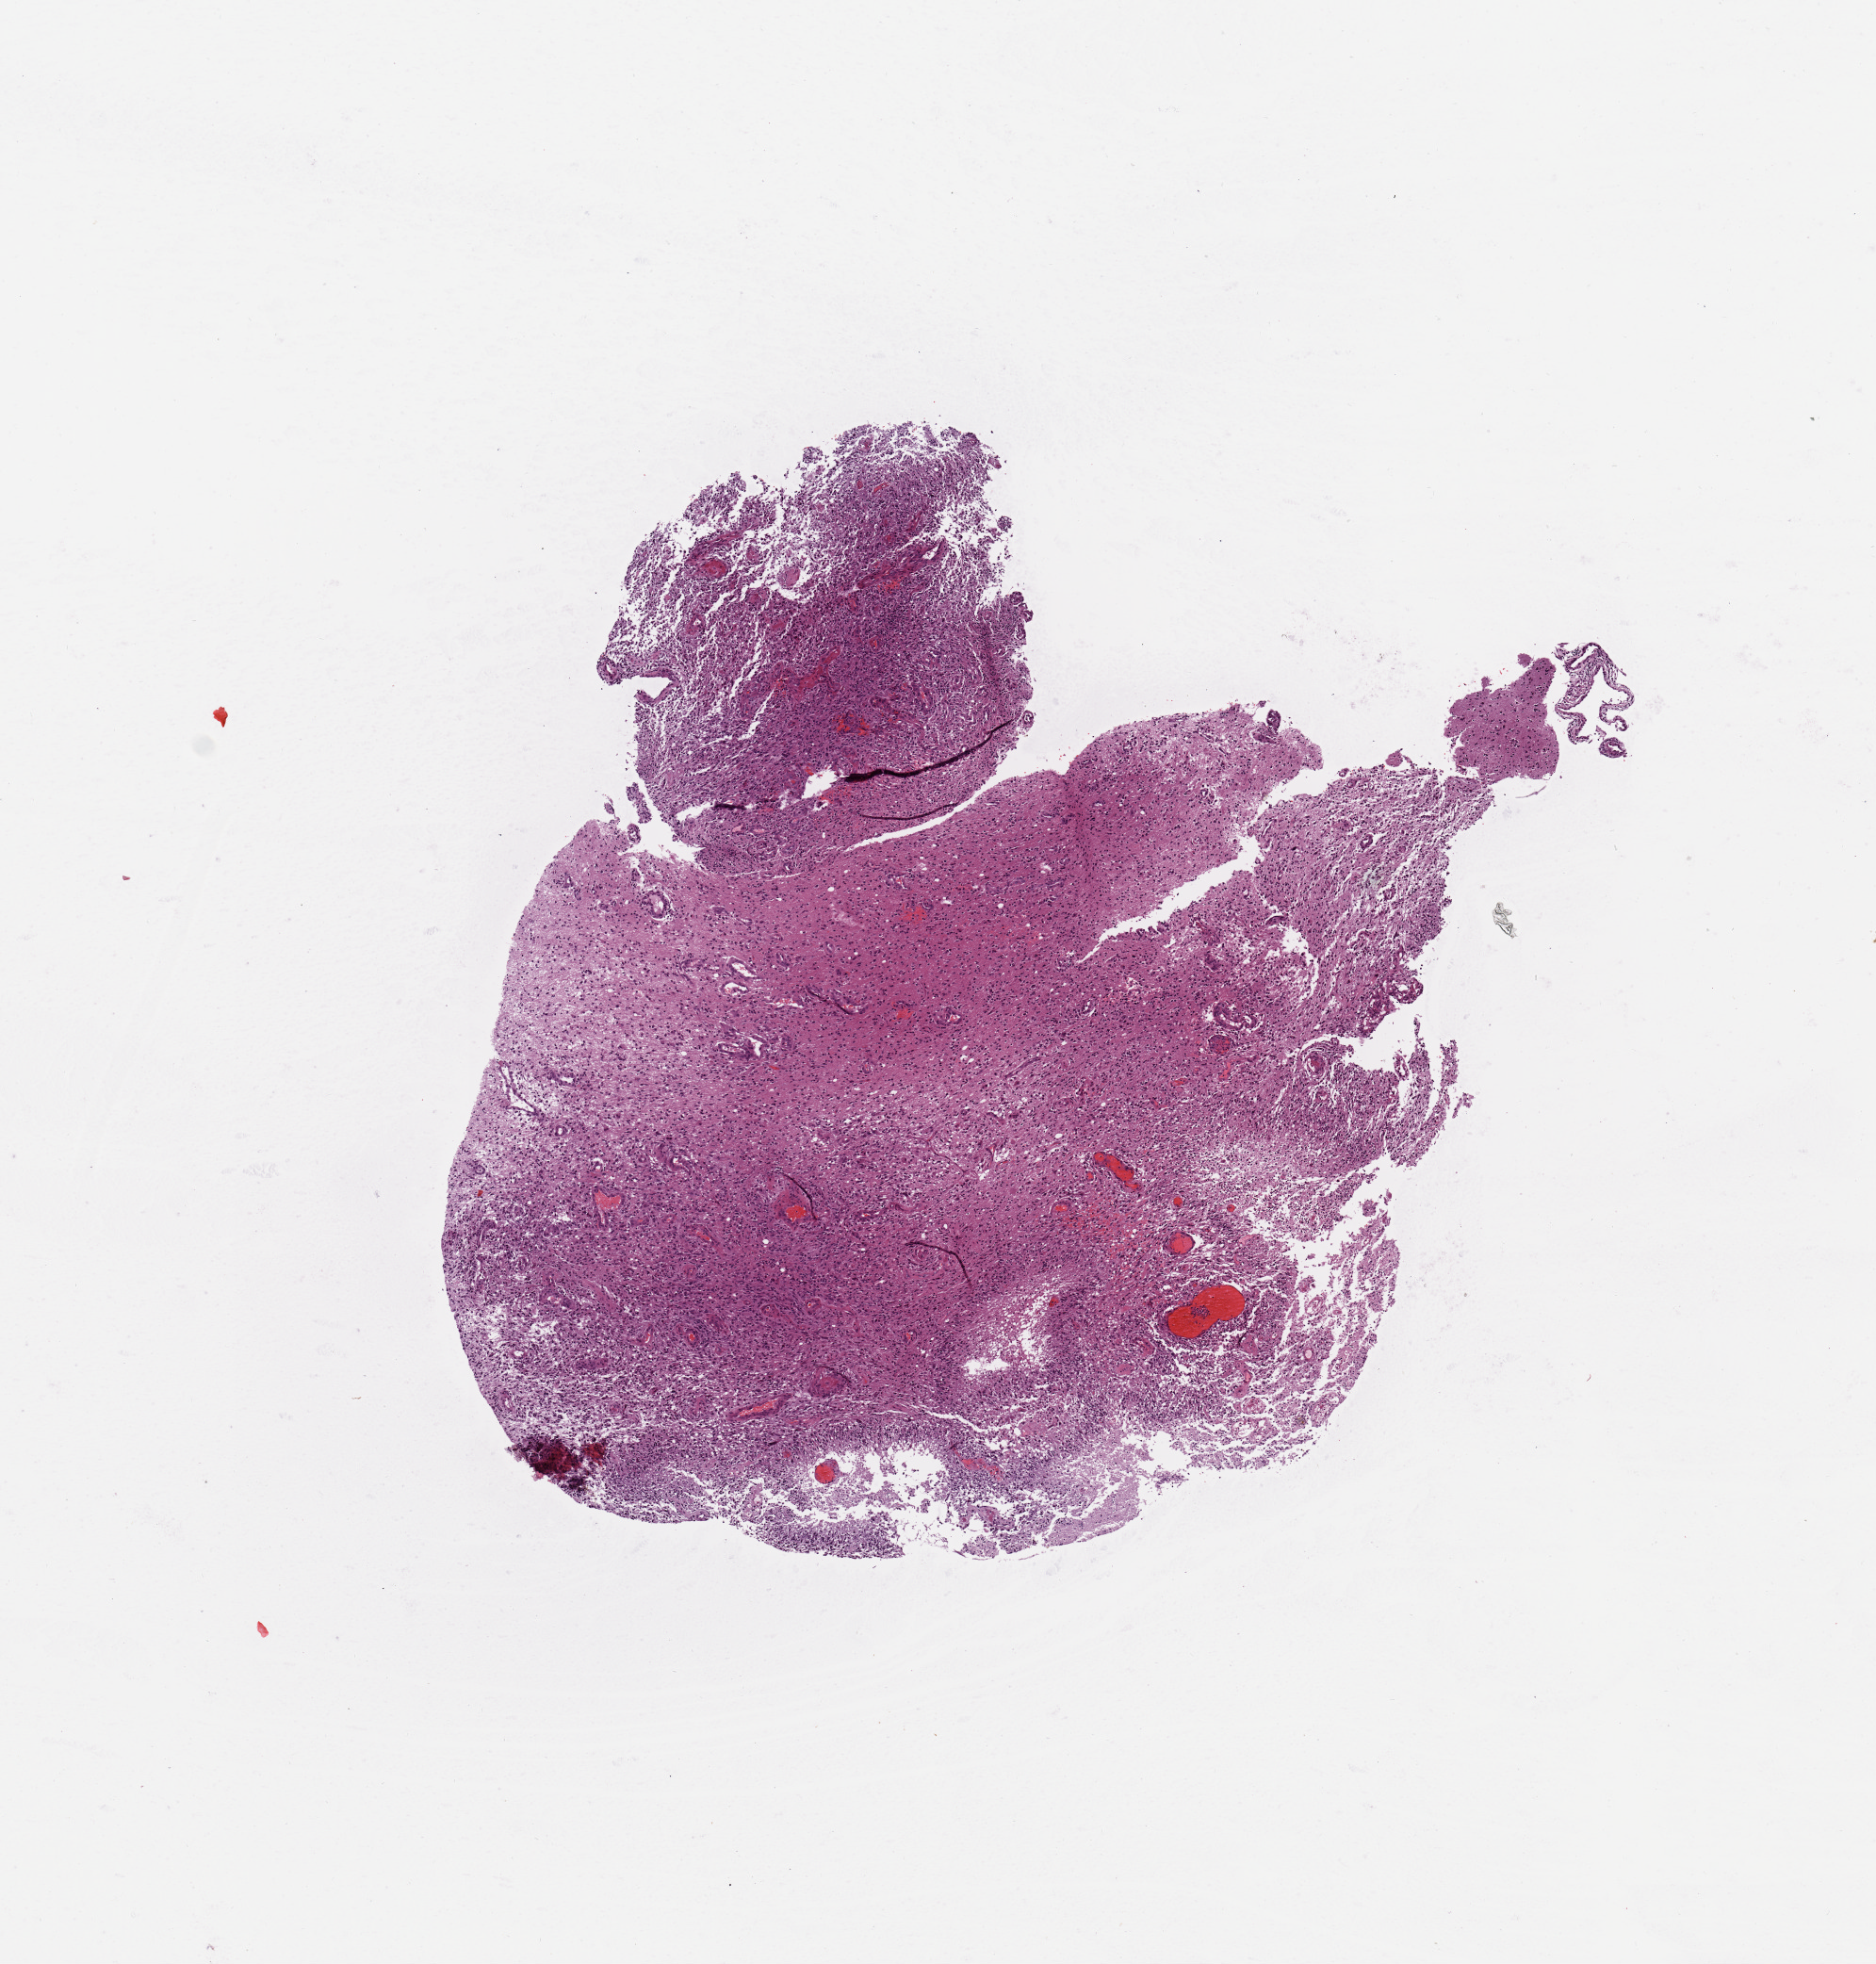
Digitized H&E tissue section (whole slide), a low-resolution overview of the entire scanned area, about 7.9 x 8.2 mm (from a 20x scan); tumour tissue sample, sampled site: occipital cortex. 53-year-old male patient. Slide review estimates, as recorded: tumour nuclei 80%, necrosis 7%.
Diagnosis: Glioblastoma. Primary tumour site (as recorded): occipital lobe.